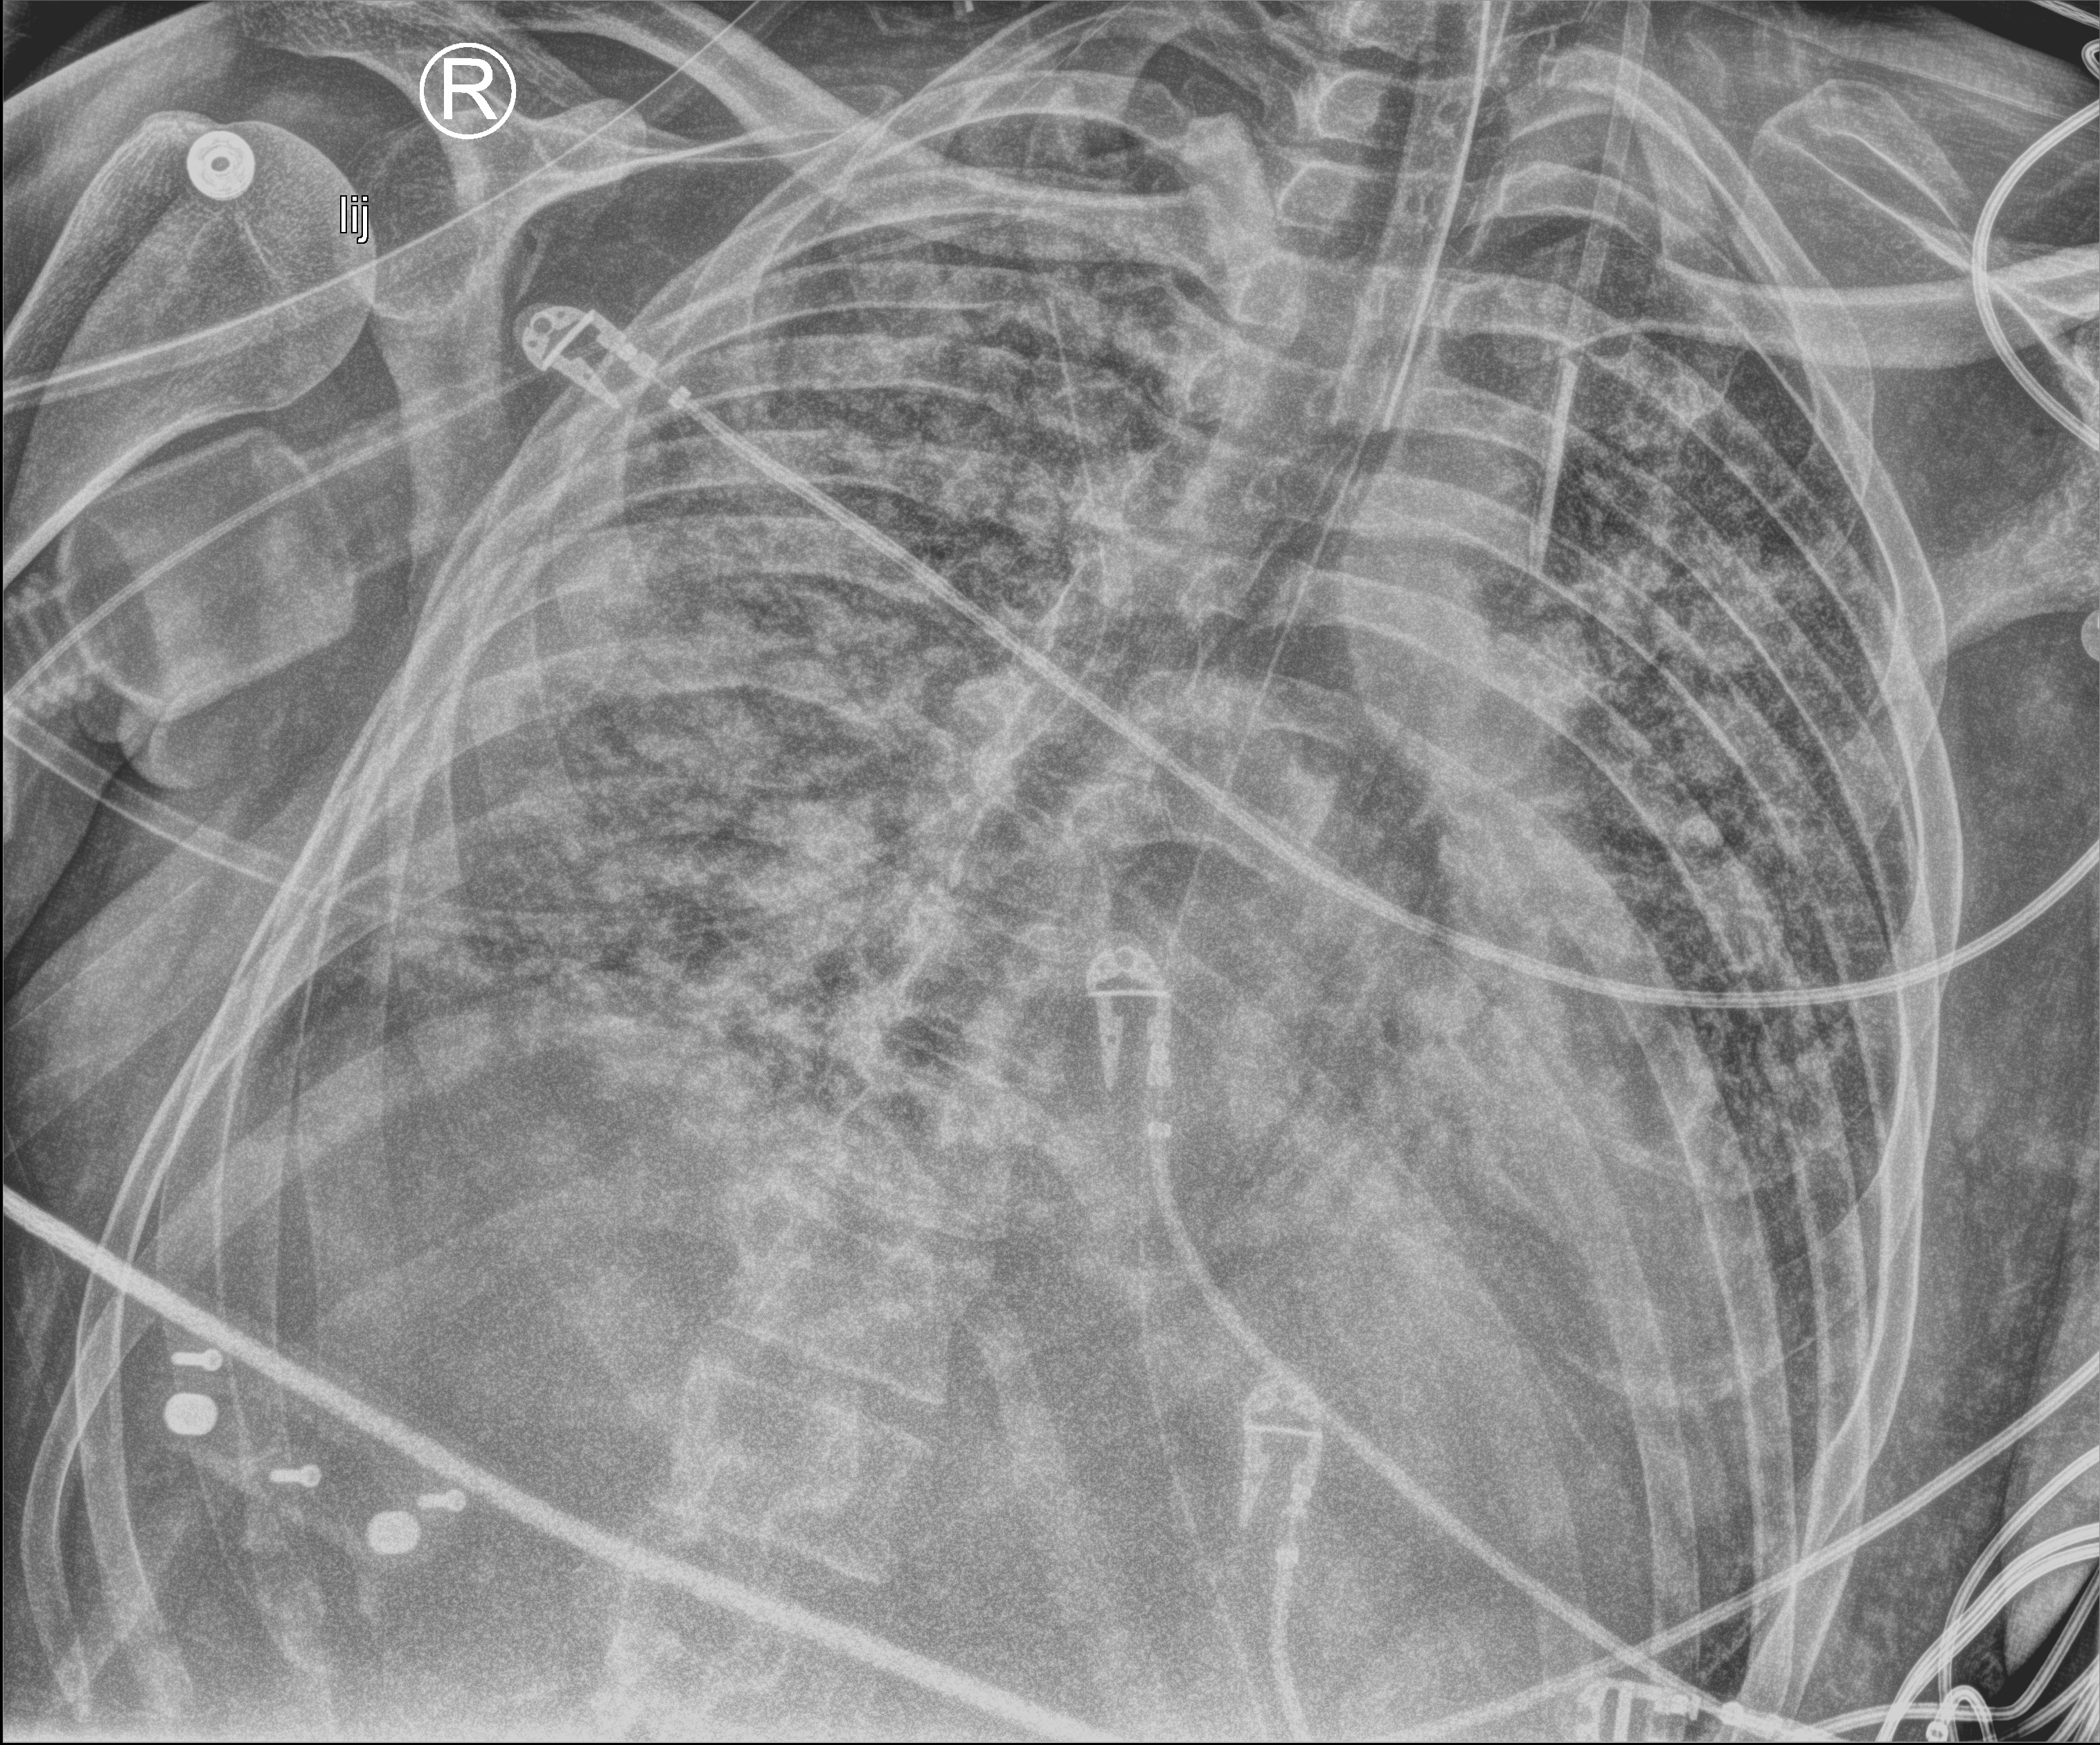
Chest X-ray (portable), anteroposterior (AP) projection. Patient hospitalised with COVID-19; male, aged 18–59 years.
Hospital-stay facts (about this admission, not read from this image; timing relative to this image not recorded): length of hospital stay: 75 days.